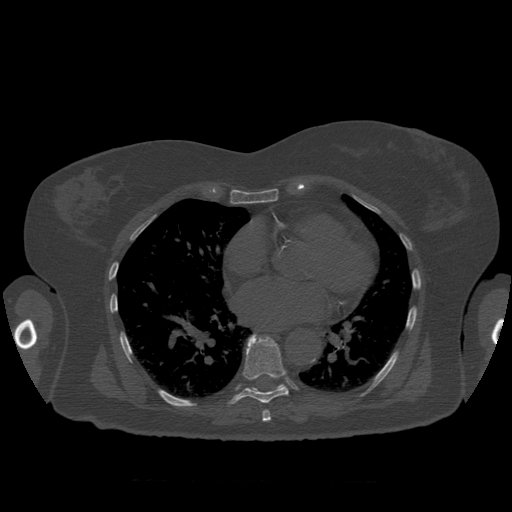
CT including the spine, one axial slice; position 376 of 399 along the scan axis; 120 kVp; bone window (W 1800 / L 400 HU); 512 × 512 image matrix, field of view 404 × 404 mm. Patient age 81 years. From the clinical record (not read from this slice): primary cancer: renal; vertebrae with lytic lesions (as recorded): L1.
Structures marked on this image (semi-automatically segmented with operator editing):
- T7 vertebra: box from (x=263, y=410) to (x=271, y=422) px
- T8 vertebra: (x=227, y=334)–(x=289, y=406)
- T9 vertebra: (x=280, y=384)–(x=285, y=386)